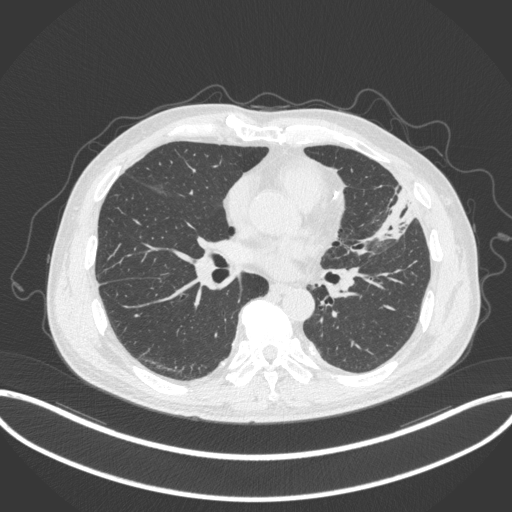
Chest CT, one axial slice; slice 159 of 382 in the series (ordered by position); reconstruction kernel B31f; lung window (W 1500 / L -600 HU); 1 mm slice thickness; 512 × 512 image matrix, field of view 415 × 415 mm. Male patient, age 64 years. Case-level facts recorded for this patient, not image findings: clinical TNM (as recorded): T4 N1 M0; histopathological grade: G3.
Outlined on this slice (bounding box drawn by a radiologist):
- lung tumour (recorded histology: adenocarcinoma): box from (x=373, y=187) to (x=416, y=250) px